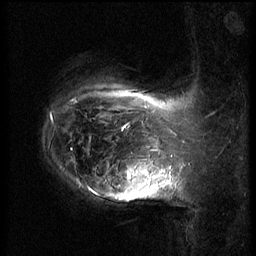
Breast MRI (dynamic contrast-enhanced), one sagittal slice. Slice 51 of 62 in the series (ordered by position). 3 images stored at this slice position (order not interpretable as contrast timing). 1.5 T. TE 4.2 ms, TR 8.9 ms. 2.5 mm slice thickness. 256 × 256 image matrix. Patient: female, 37 years. Case-level facts recorded for this patient, not image findings: setting: breast cancer imaged before/during neoadjuvant chemotherapy; receptor status: triple-negative.
Structures marked on this image (semi-automatically segmented with operator editing):
- analysis volume of interest (the breast-tissue region the enhancement analysis was run in; not a lesion): bounding box <116,146,168,203> (left, top, right, bottom; pixels)
- tumour enhancement mask (voxels above the 140 % enhancement threshold inside the analysis volume of interest): <128,169,168,177>